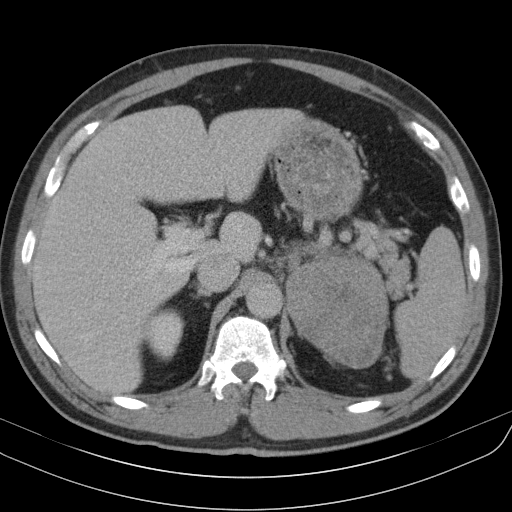
Contrast-enhanced abdominal CT, one axial slice. Slice 72 of 91 in the series (ordered by position). 130 kVp. Soft-tissue window (W 400 / L 40 HU). 512 × 512 image matrix, field of view 370 × 370 mm. Patient: male, 51 years. From the clinical record (not read from this slice): diagnosis: adrenocortical carcinoma; tumour side: left adrenal.
Structures marked on this image (semi-automatic segmentation, software-assisted and operator-edited):
- mass: box from (x=287, y=254) to (x=389, y=366) px